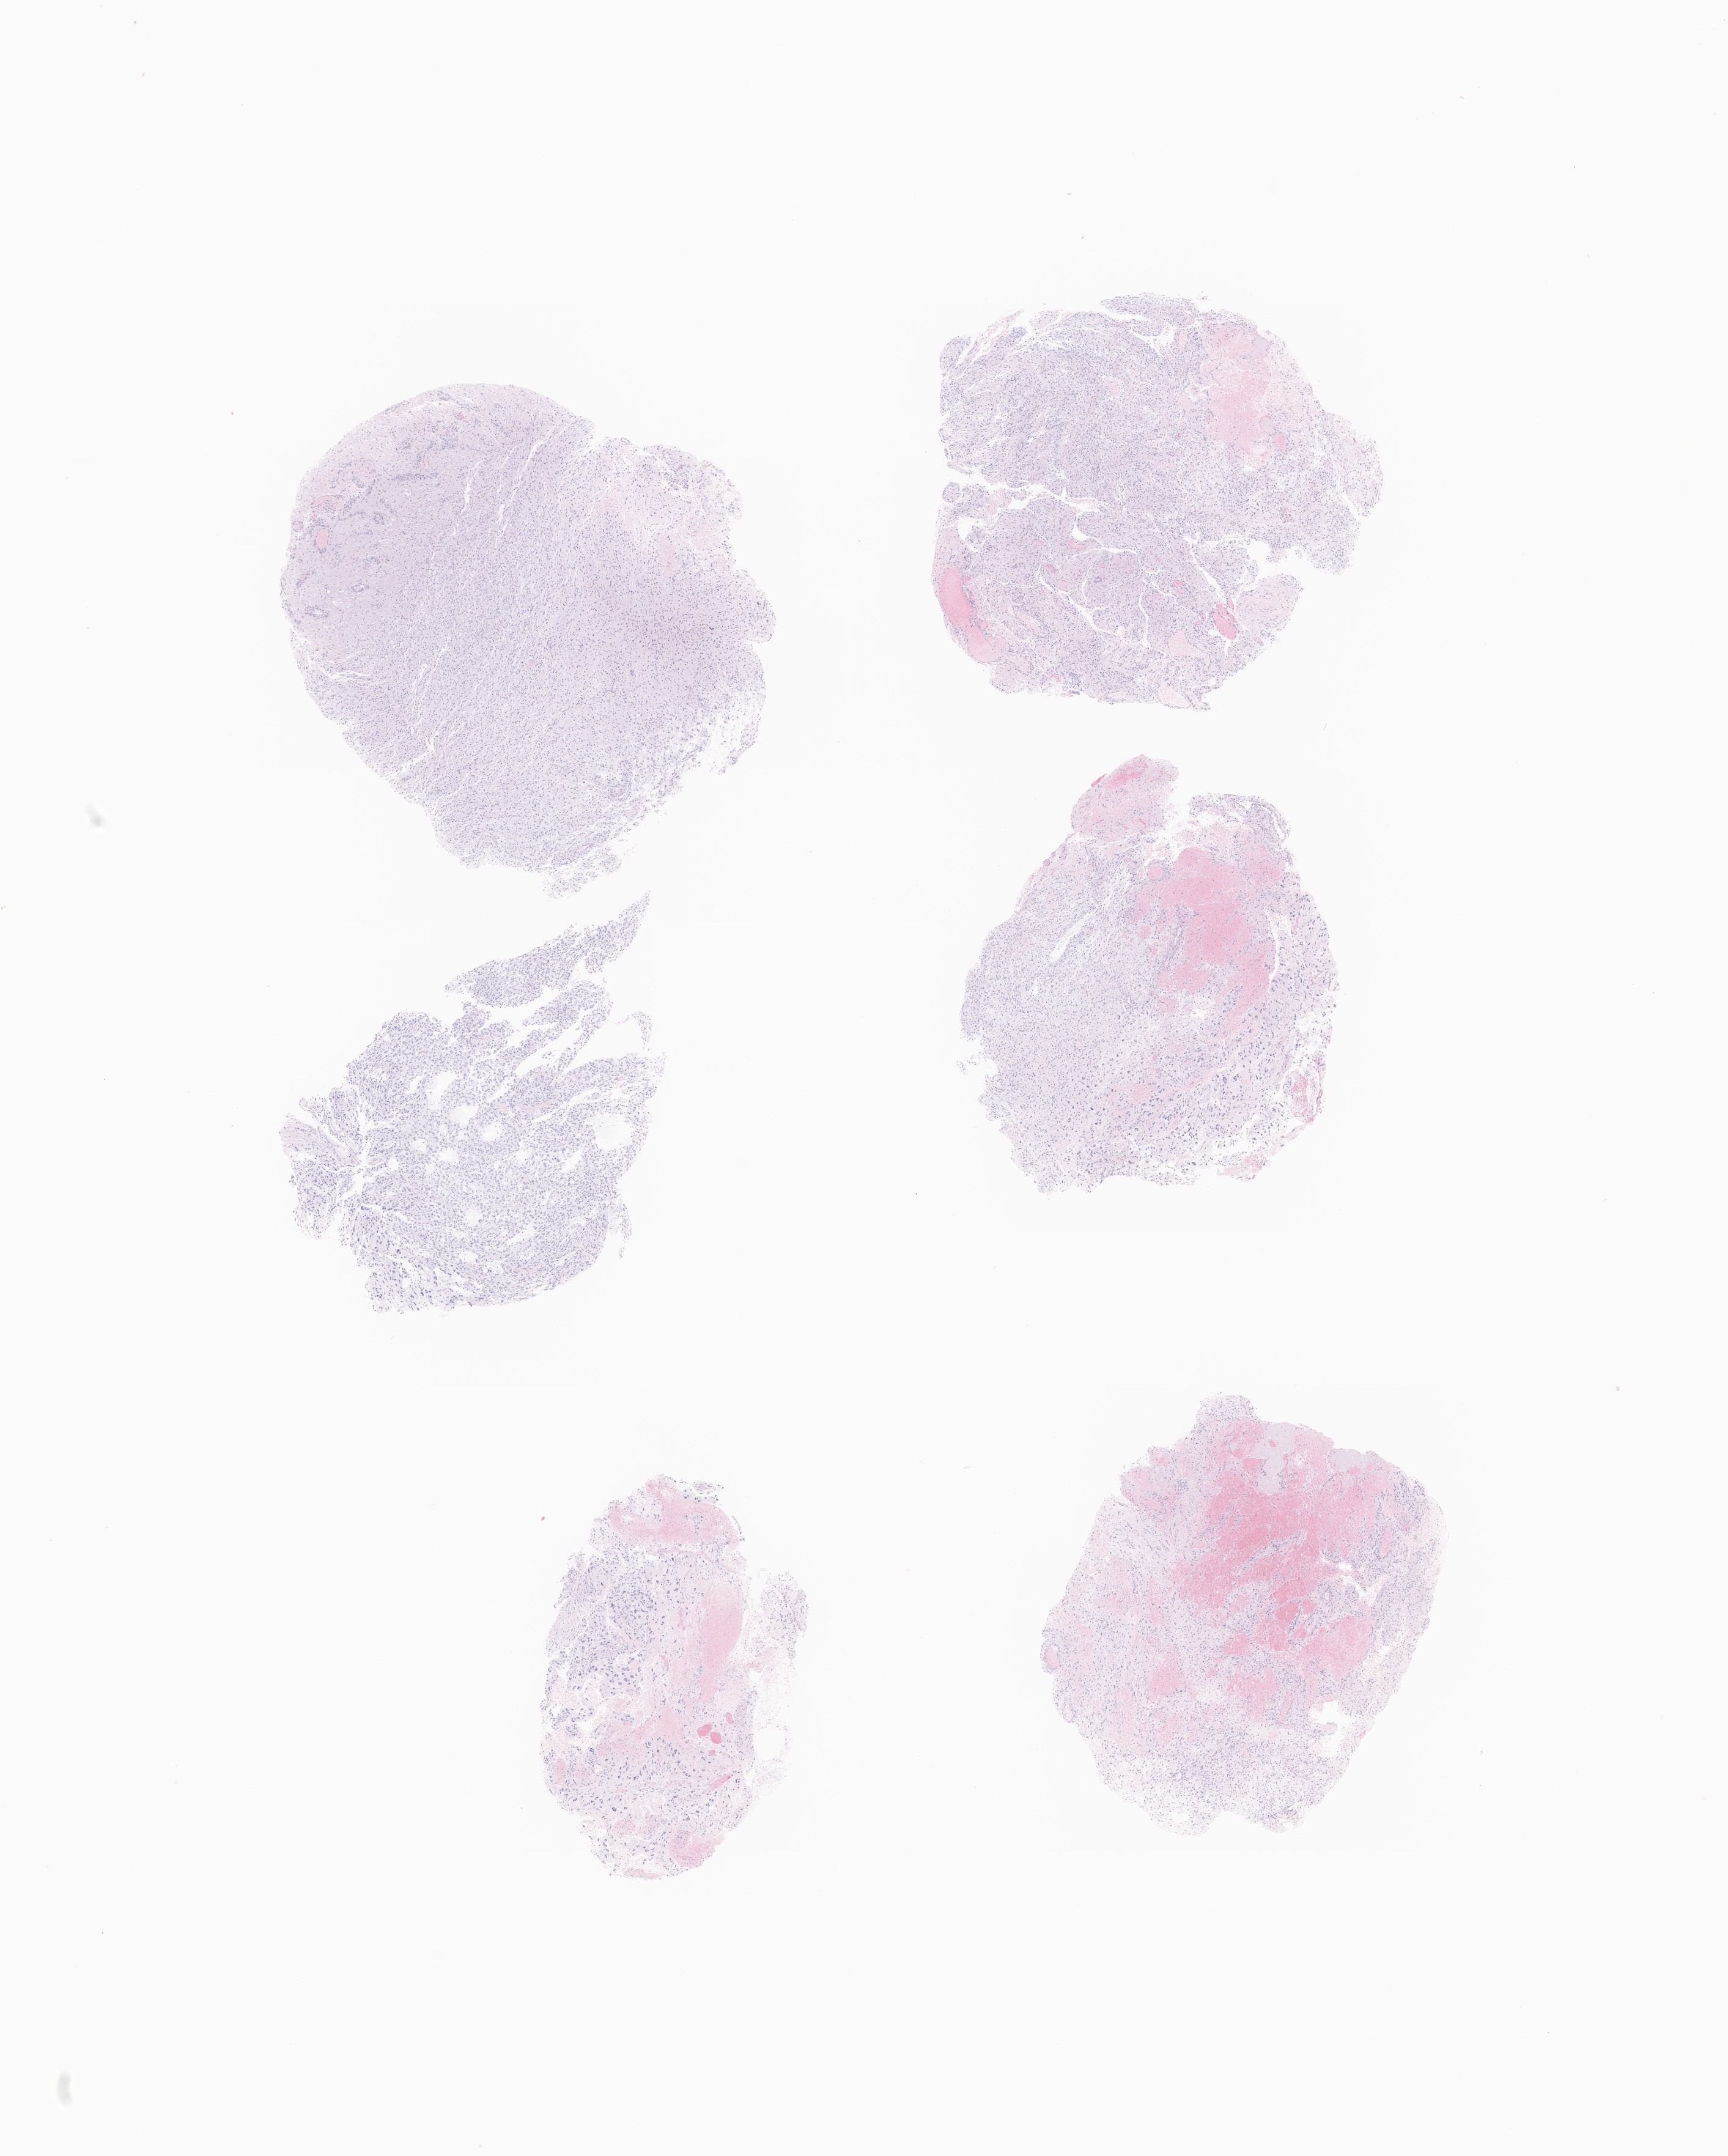
H&E whole-slide image of tumor tissue from the brain — a low-resolution overview of the entire scanned area, about 11.9 x 14.9 mm. FFPE section. Patient: male, age 167 months (13 years 11 months).
Recorded diagnosis: Glioma, malignant.